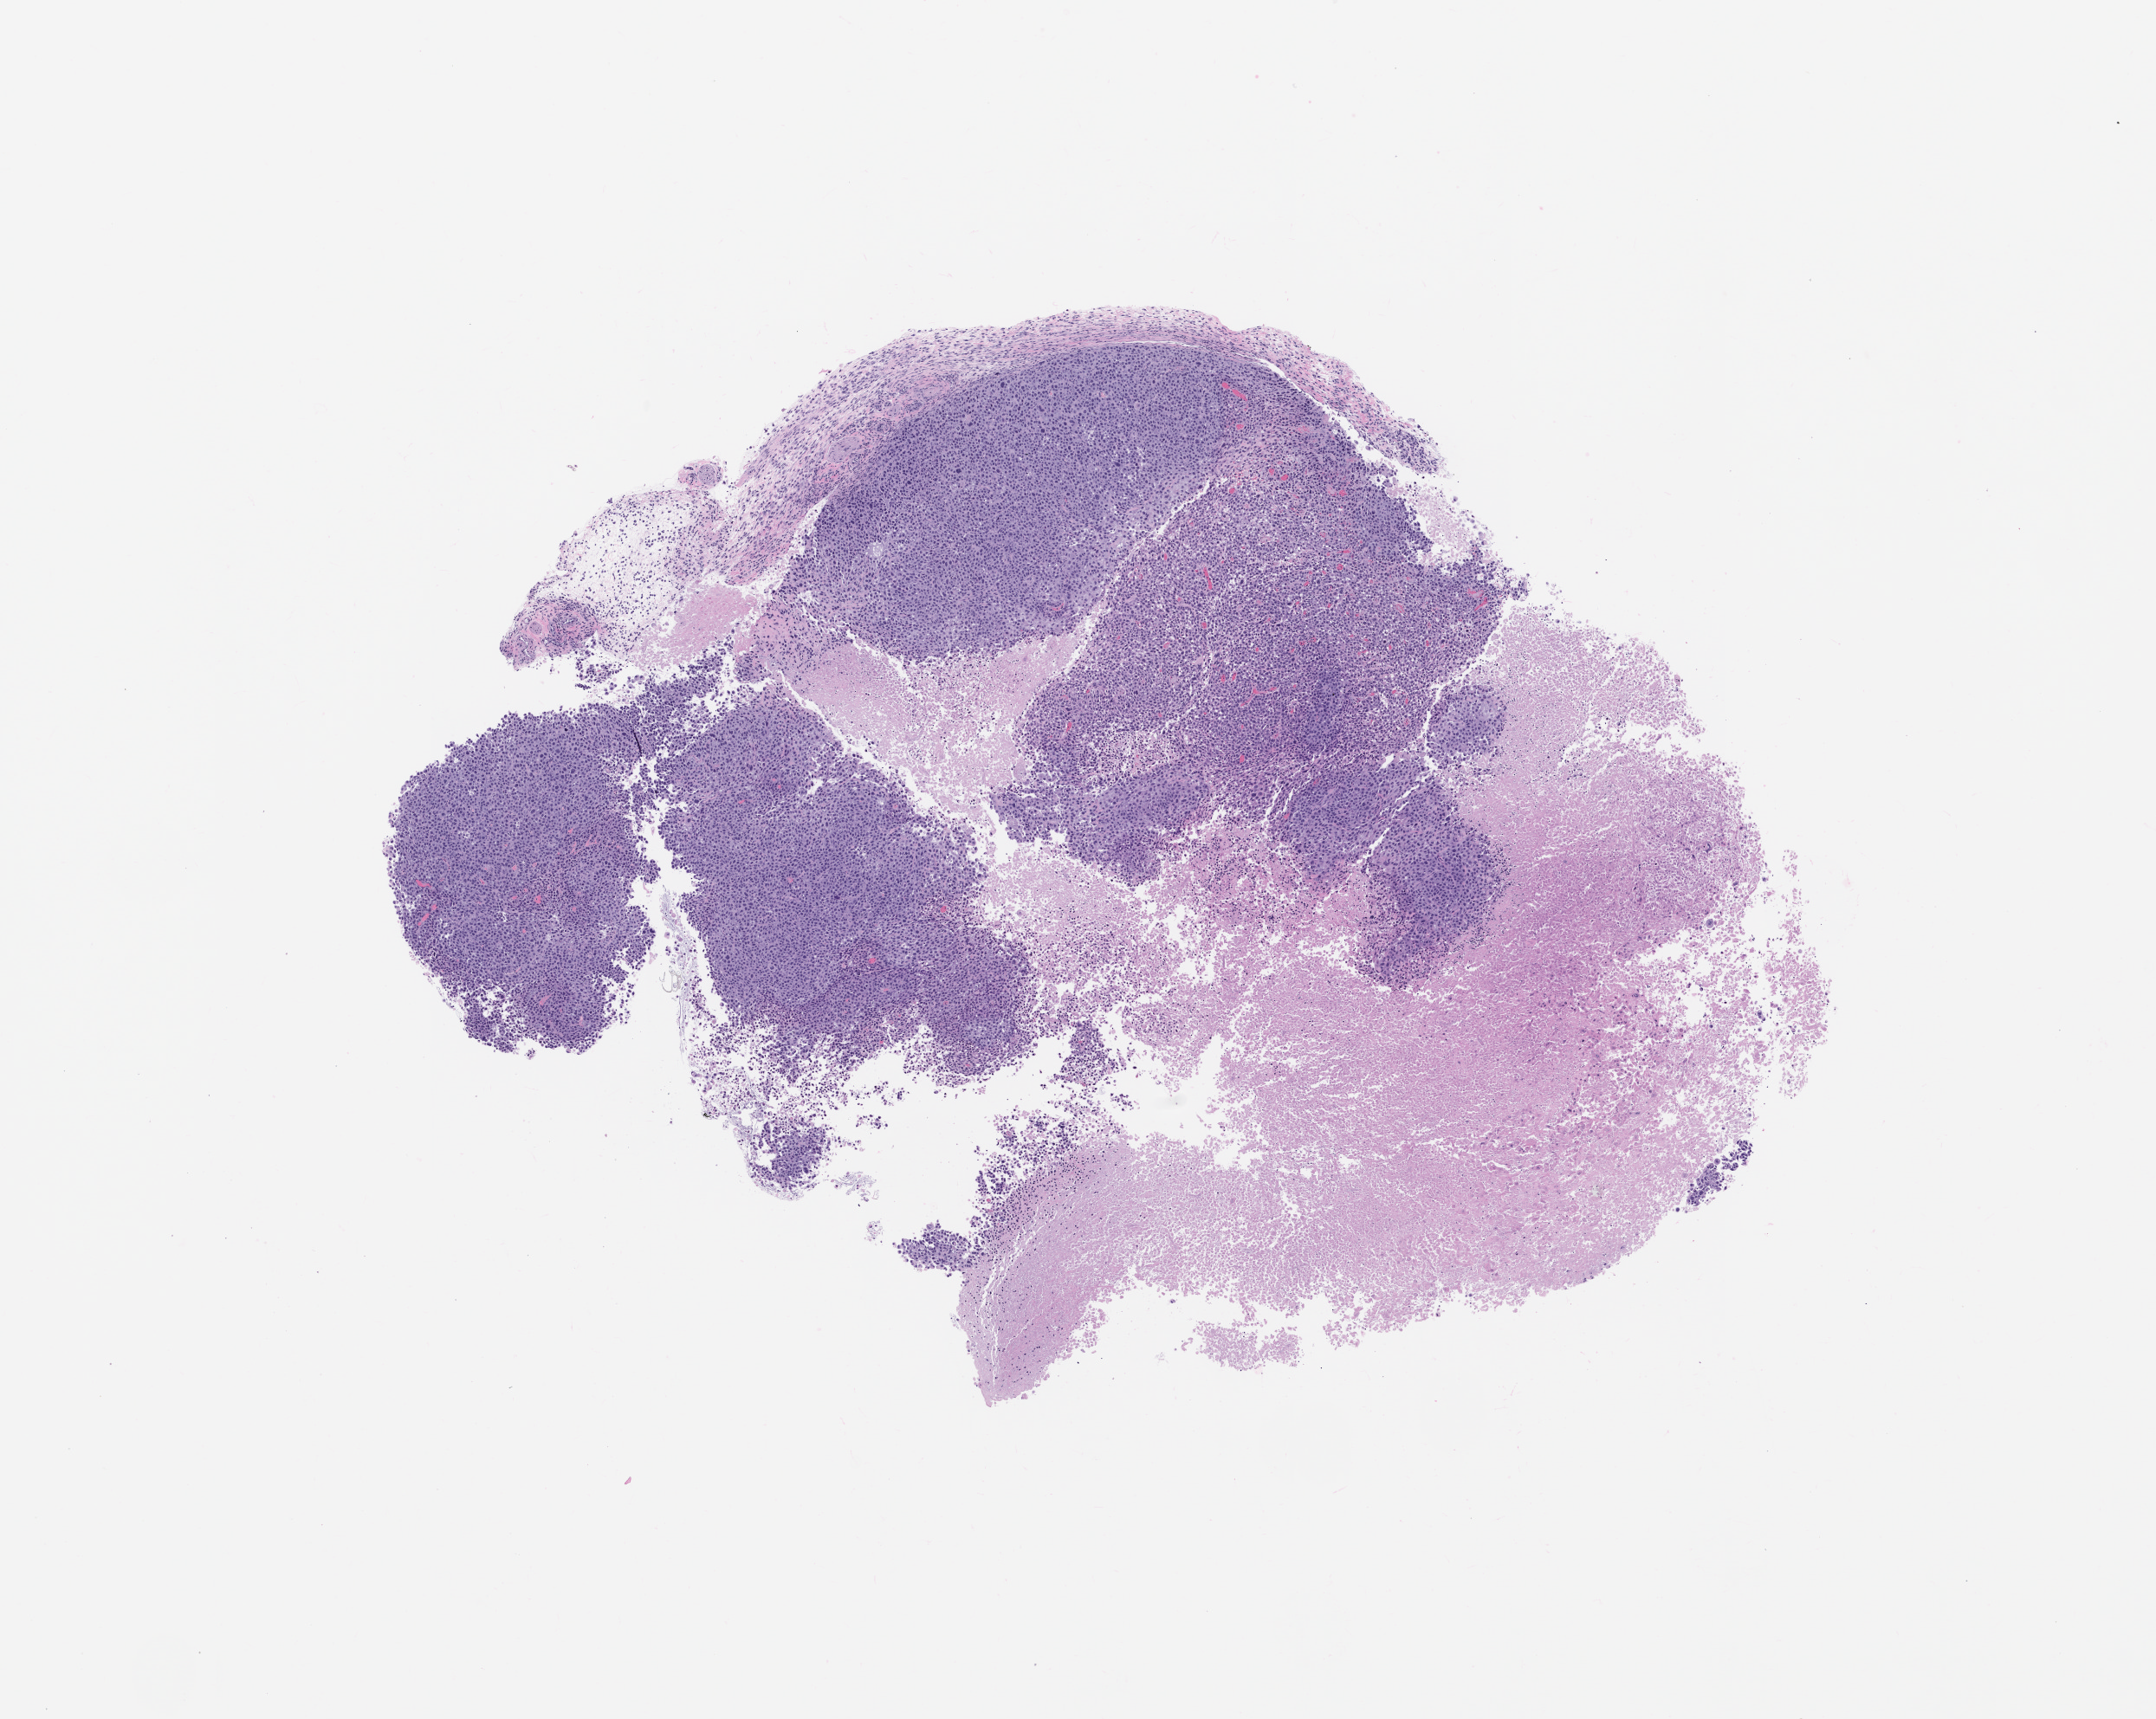
Hematoxylin and eosin (H&E) whole-slide image of a patient-derived xenograft (PDX) tumor grown in a mouse, passage 0 — shown as a low-resolution overview of the whole scanned area (about 10.0 x 8.0 mm); formalin-fixed, paraffin-embedded (FFPE) tissue; originating tumor site category: head and neck.
Originating patient diagnosis: Head and Neck Squamous Cell Carcinoma.